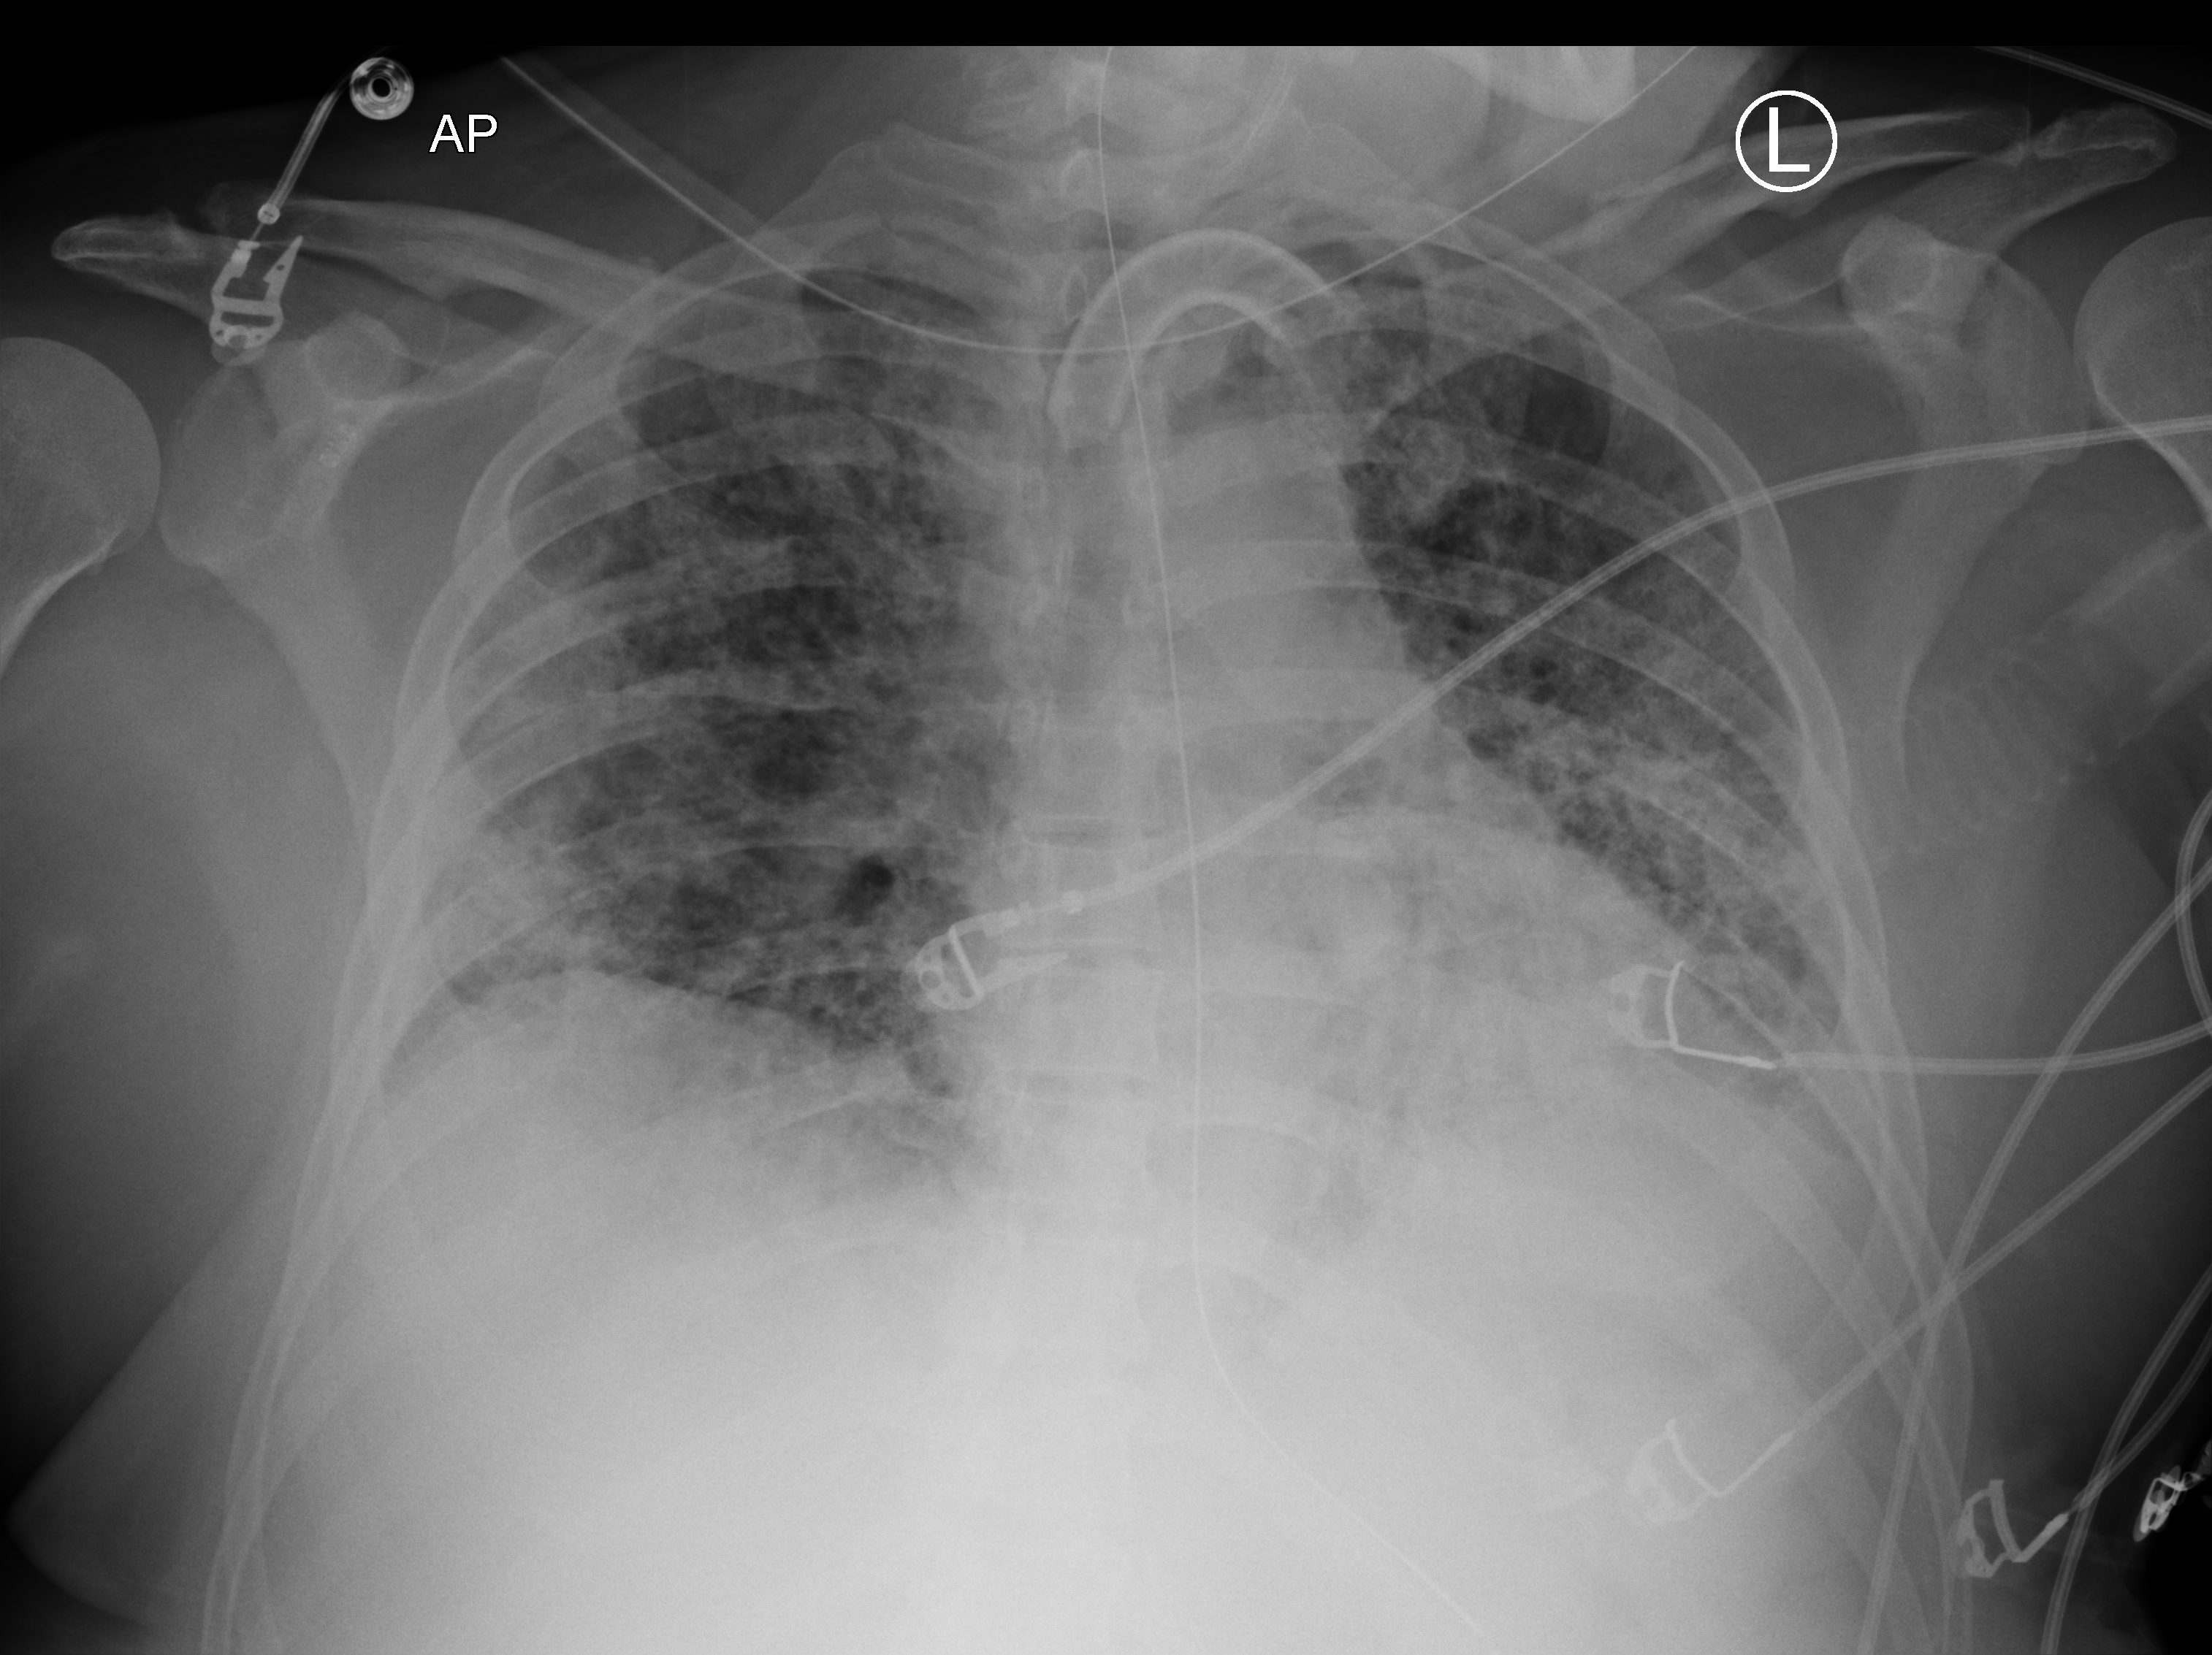
Portable chest radiograph; anteroposterior (AP) projection. Male patient hospitalised with COVID-19, age 18–59 years.
Admission-level facts for this patient (not findings on this image; timing relative to this image not recorded): mechanically ventilated during this hospital stay: yes.